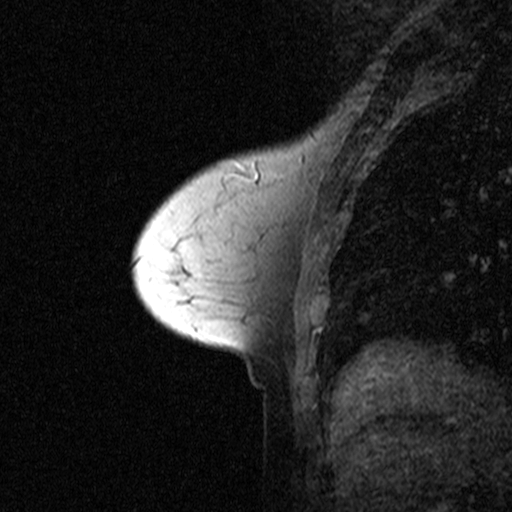
Breast MRI (dynamic contrast-enhanced), one sagittal slice. Position 16 of 44 along the scan axis. Dynamic contrast-enhanced study with each time point stored as its own series, time point 2 of 3 at this slice position (early post-contrast, ordered by acquisition time). 1.5 T. TE 4.5 ms, TR 11 ms. 3 mm slice thickness. 512 × 512 image matrix. Female patient, age 53 years. Case-level facts recorded for this patient, not image findings: setting: breast cancer imaged before/during neoadjuvant chemotherapy; receptor status: HR-positive, HER2-negative.
Outlined on this slice (semi-automatically segmented with operator editing):
- analysis volume of interest (the breast-tissue region the enhancement analysis was run in; not a lesion): box from (x=170, y=150) to (x=277, y=273) px
- tumour enhancement mask (voxels above the 90 % enhancement threshold inside the analysis volume of interest): (x=223, y=176)–(x=256, y=181)